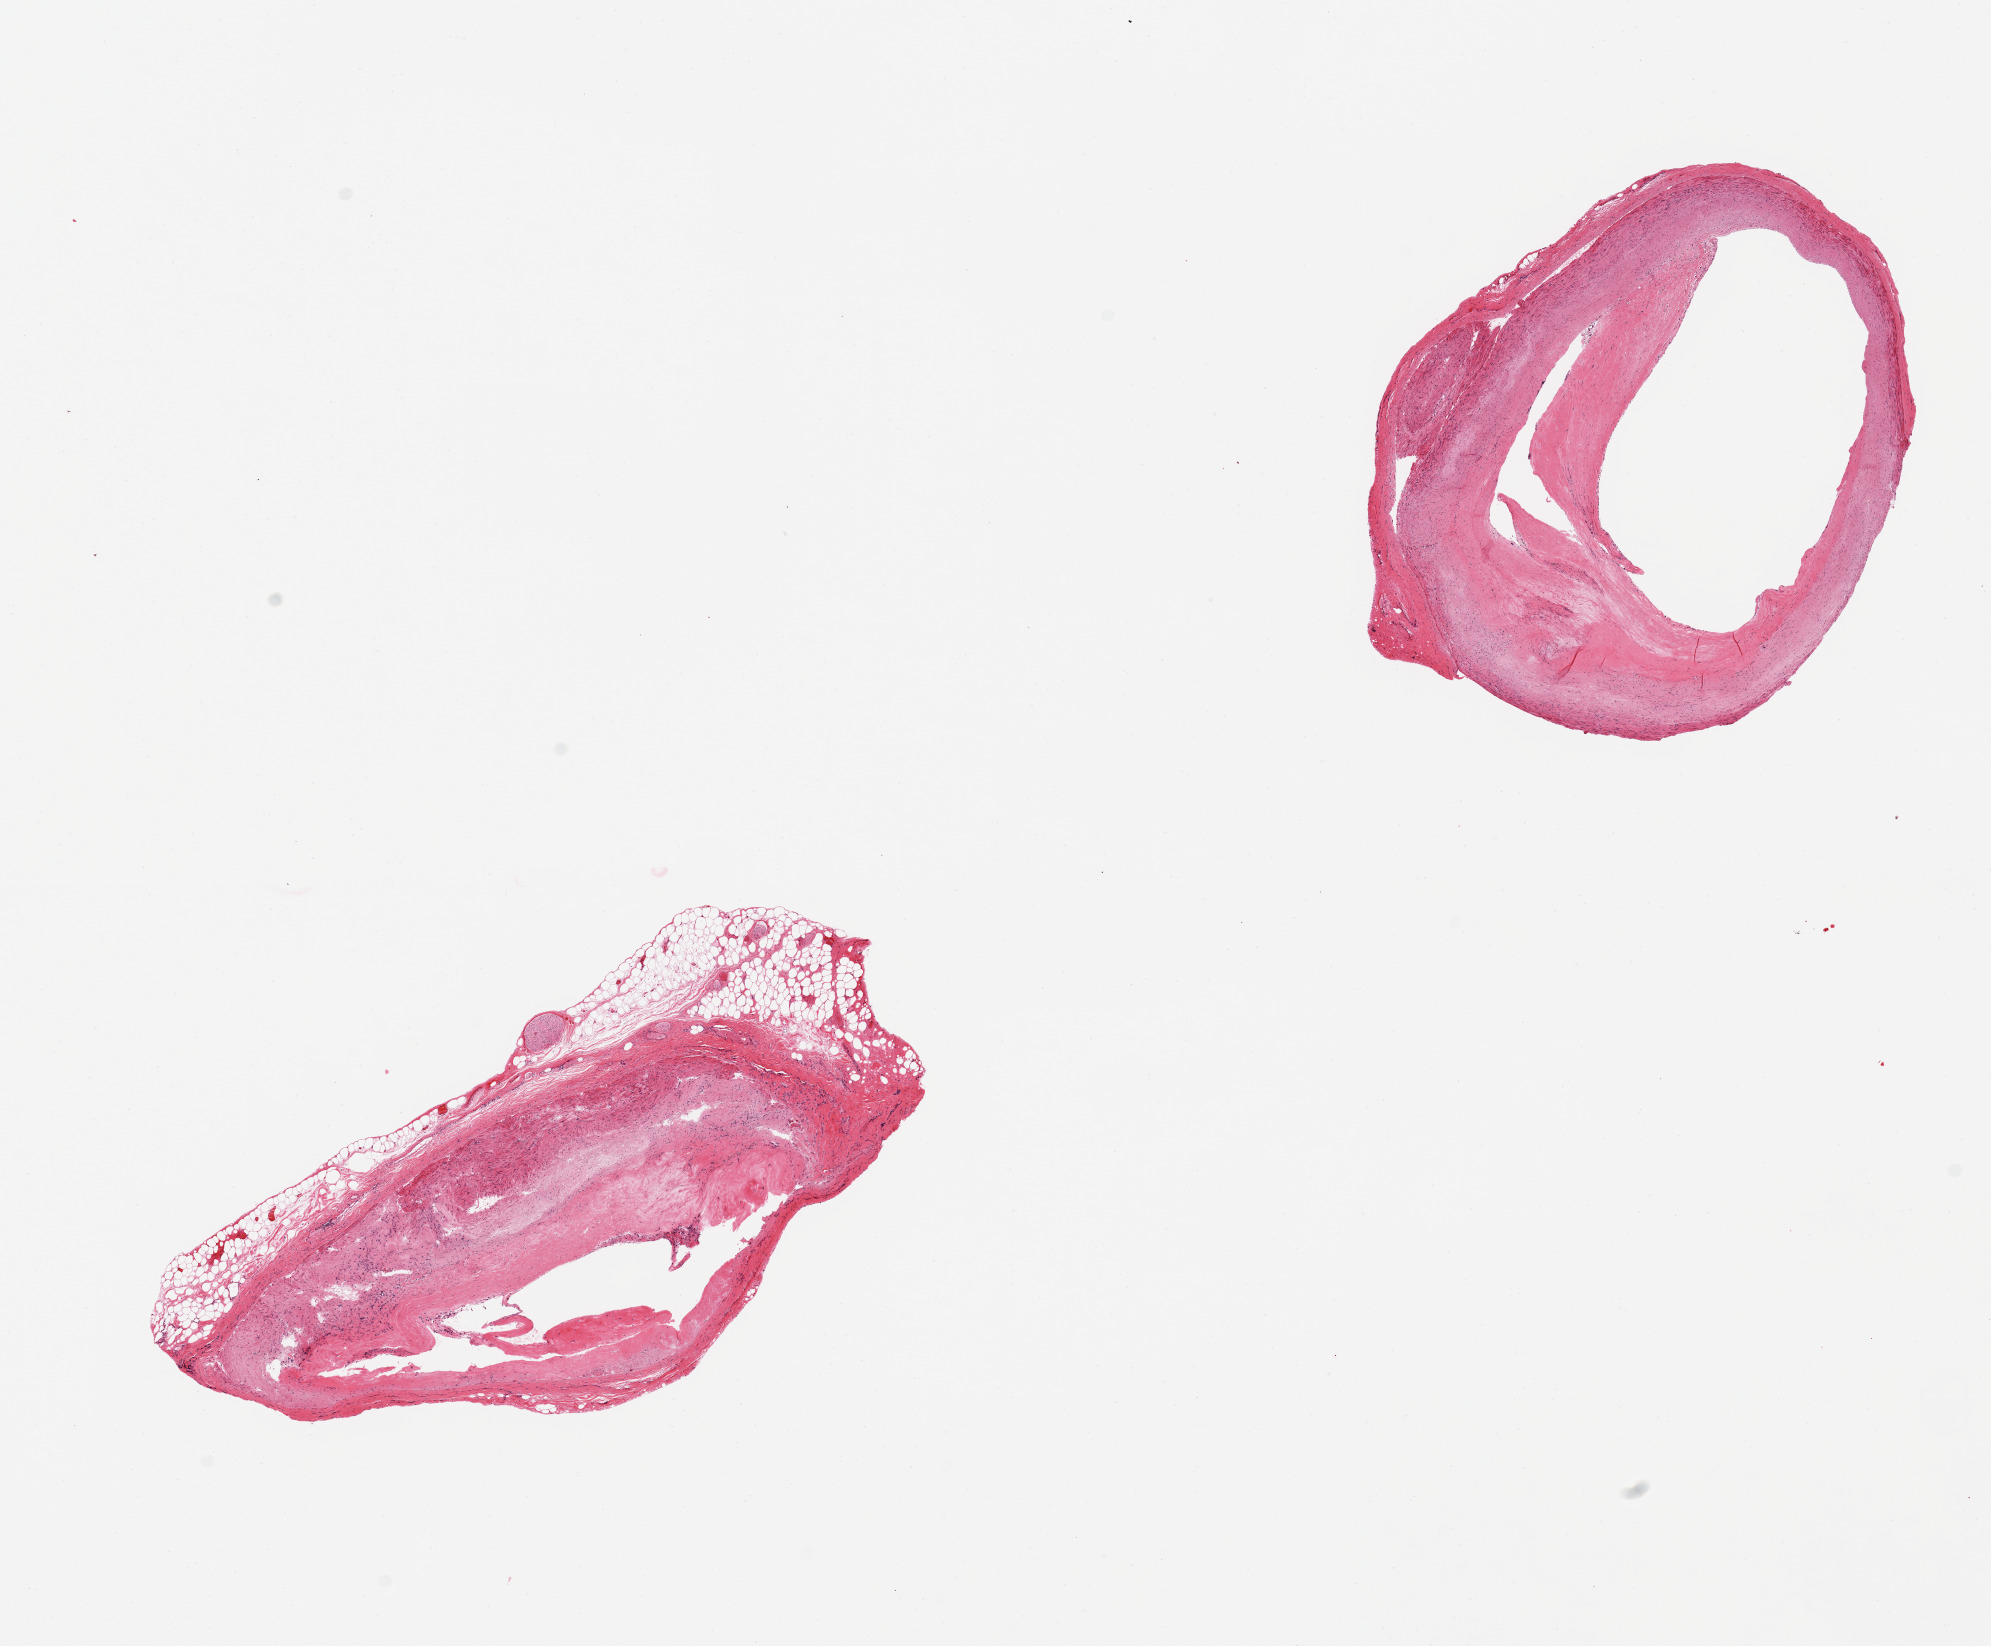
Whole-slide image, hematoxylin and eosin (H&E) stain, a low-resolution overview of the entire scanned area, about 15.8 x 13.0 mm; PAXgene-fixed paraffin-embedded (PFPE) section; target tissue: coronary artery; tissue donor sample.
• pathologist's review note for this sample: 2 pieces, calcific atherosclerosis, one piece is ~25% attached fat/nerve